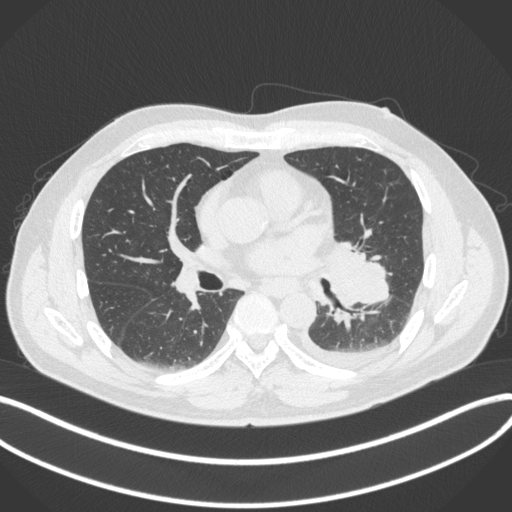
Chest CT, one axial slice; slice 188 of 350 in the series (ordered by position); reconstruction kernel B31f; lung window (W 1500 / L -600 HU); 1 mm slice thickness; 512 × 512 image matrix. Patient: male, 58 years. Case-level facts recorded for this patient, not image findings: clinical TNM (as recorded): T3 N1 M1b; histopathological grade: G3.
Annotated regions visible in this slice (bounding box drawn by a radiologist):
- lung tumour (recorded histology: small cell carcinoma): bounding box (x1, y1, x2, y2) in pixels: (319, 232, 394, 314)